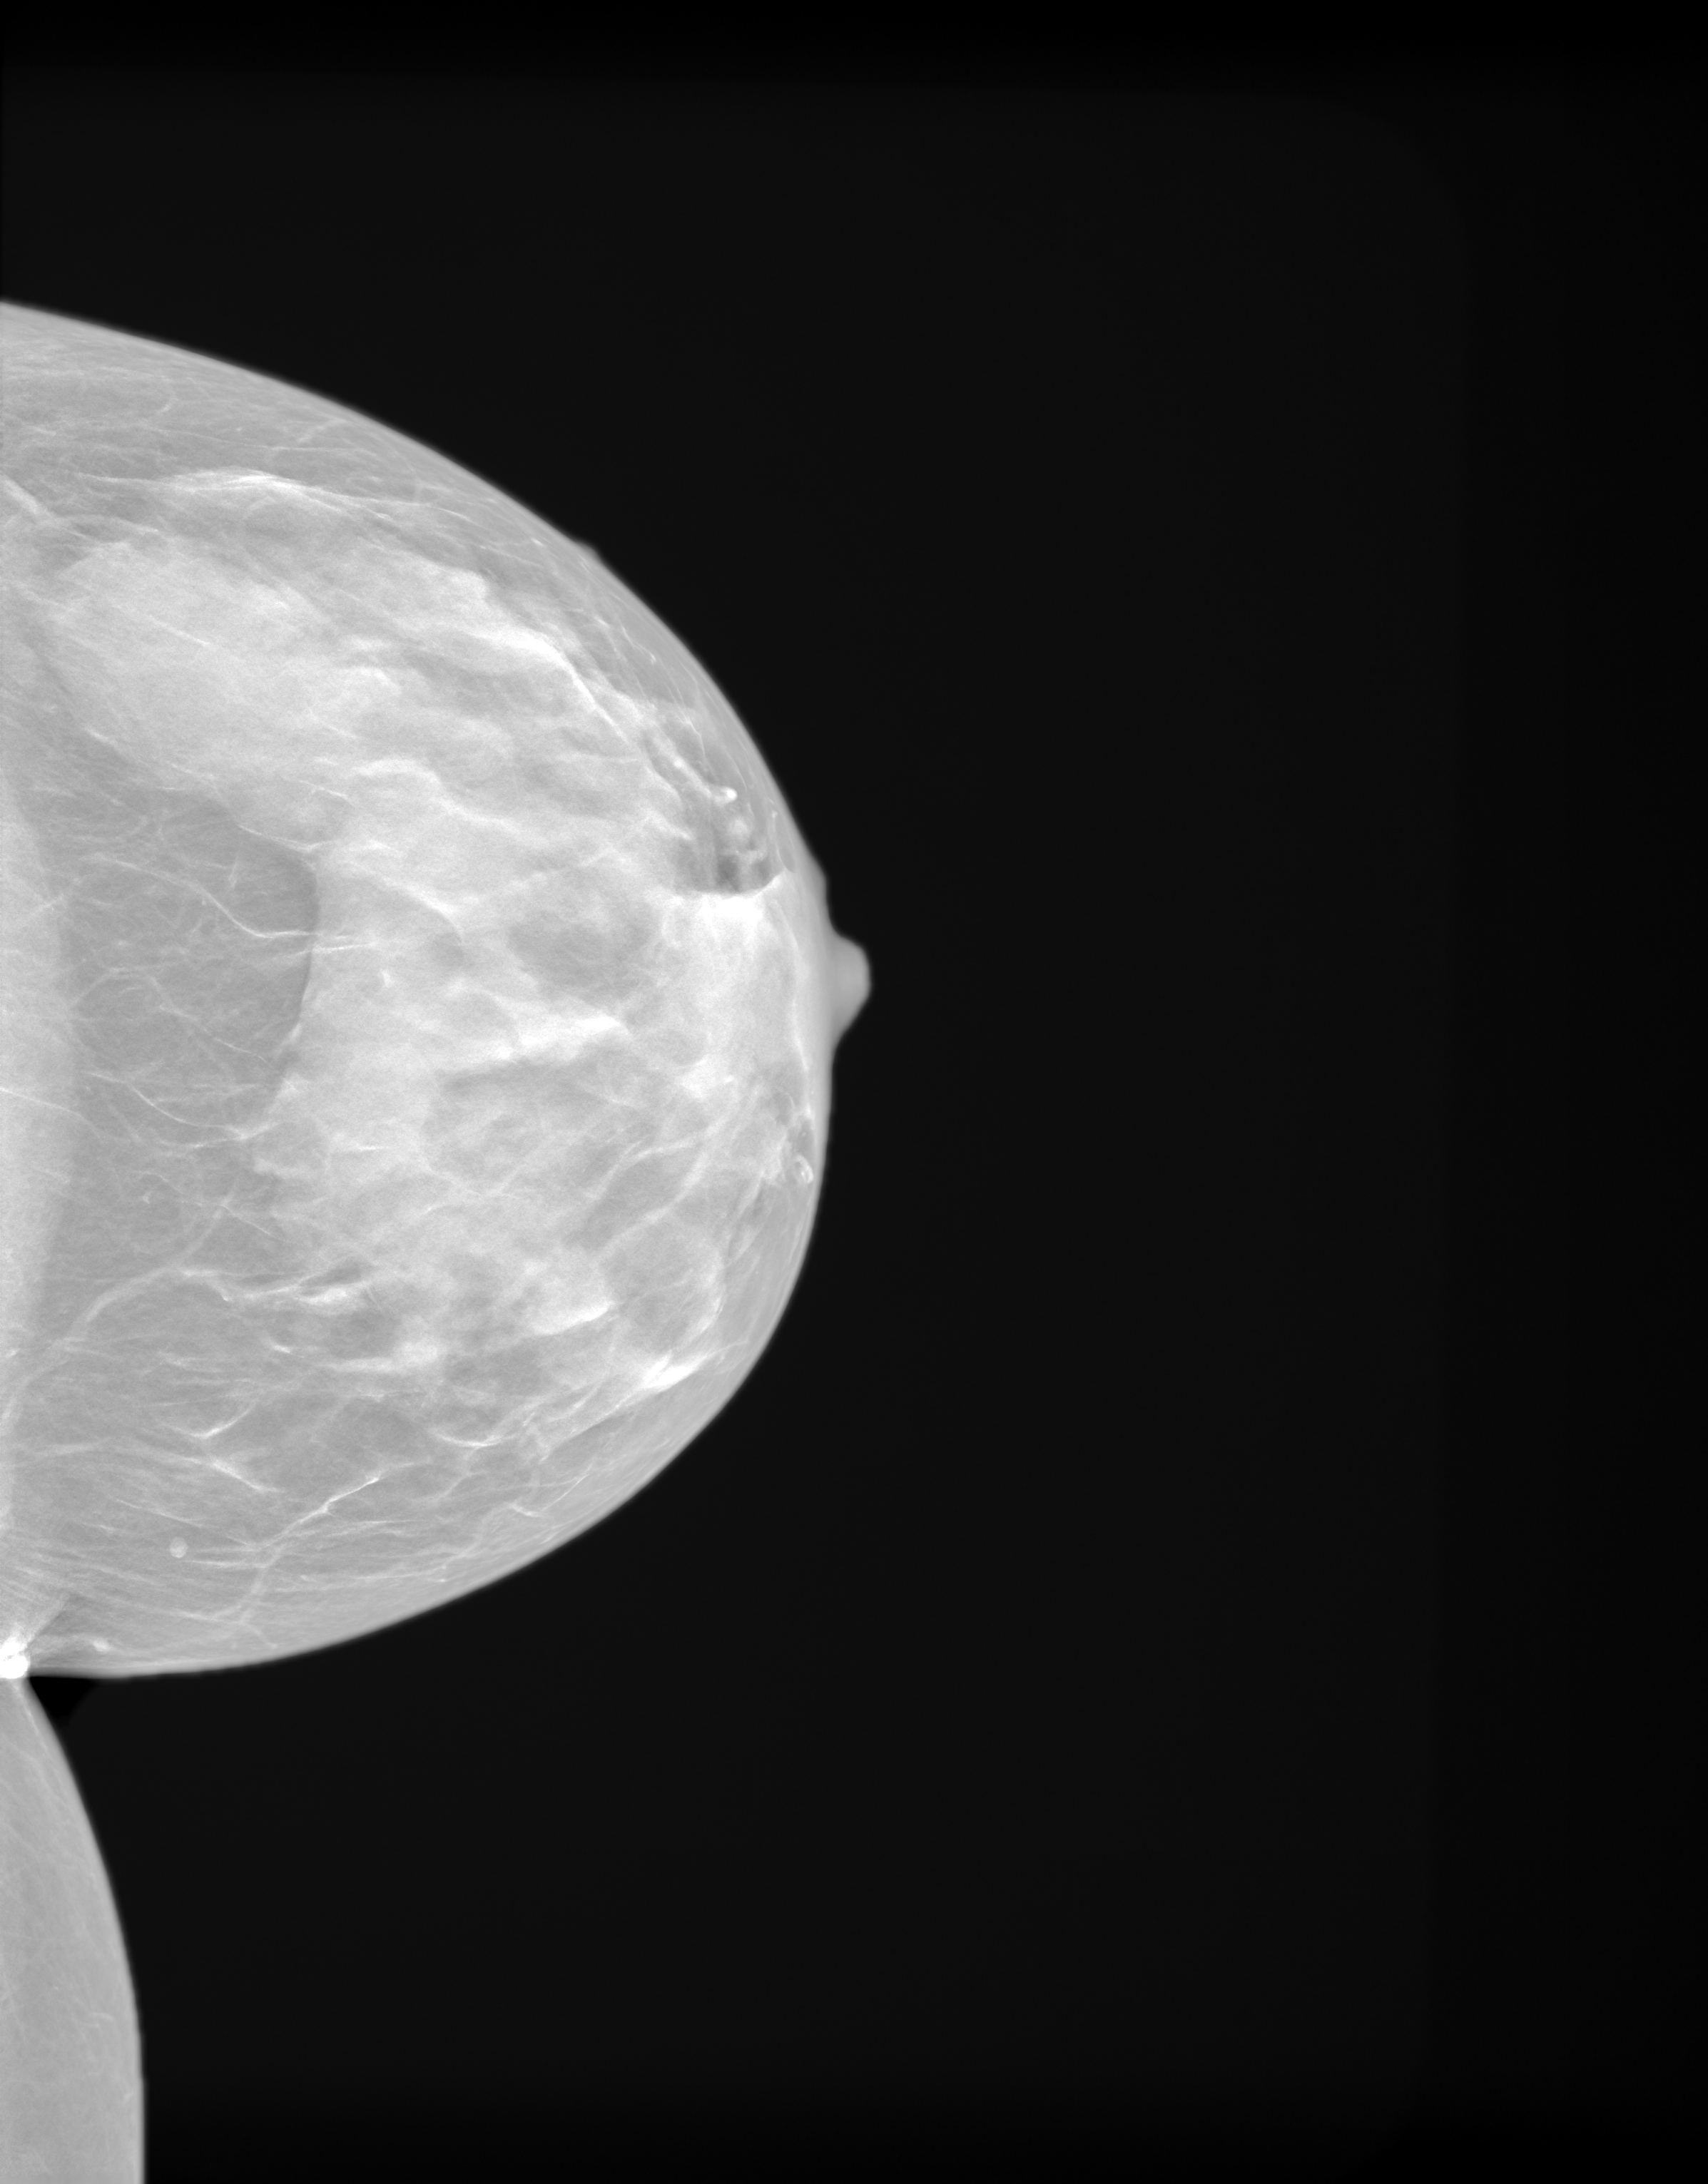
Screening examination. Female patient, age 61 years.
Image type: synthesized 2-D view from tomosynthesis. Breast: left. Projection: CC view.